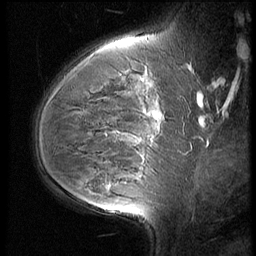
Breast MRI (dynamic contrast-enhanced), one sagittal slice; slice 41 of 60 in the series (ordered by position); 3 images stored at this slice position (order not interpretable as contrast timing); 1.5 T; TE 4.2 ms, TR 9 ms; 256 × 256 image matrix, field of view 180 × 180 mm. Patient: female, 35 years. From the clinical record (not read from this slice): setting: breast cancer imaged before/during neoadjuvant chemotherapy; receptor status: HR-positive, HER2-negative.
Structures marked on this image (semi-automatic segmentation, software-assisted and operator-edited):
- analysis volume of interest (the breast-tissue region the enhancement analysis was run in; not a lesion): bounding box [x1, y1, x2, y2] px = [56, 58, 176, 202]
- tumour enhancement mask (voxels above the 140 % enhancement threshold inside the analysis volume of interest): [146, 113, 159, 119]